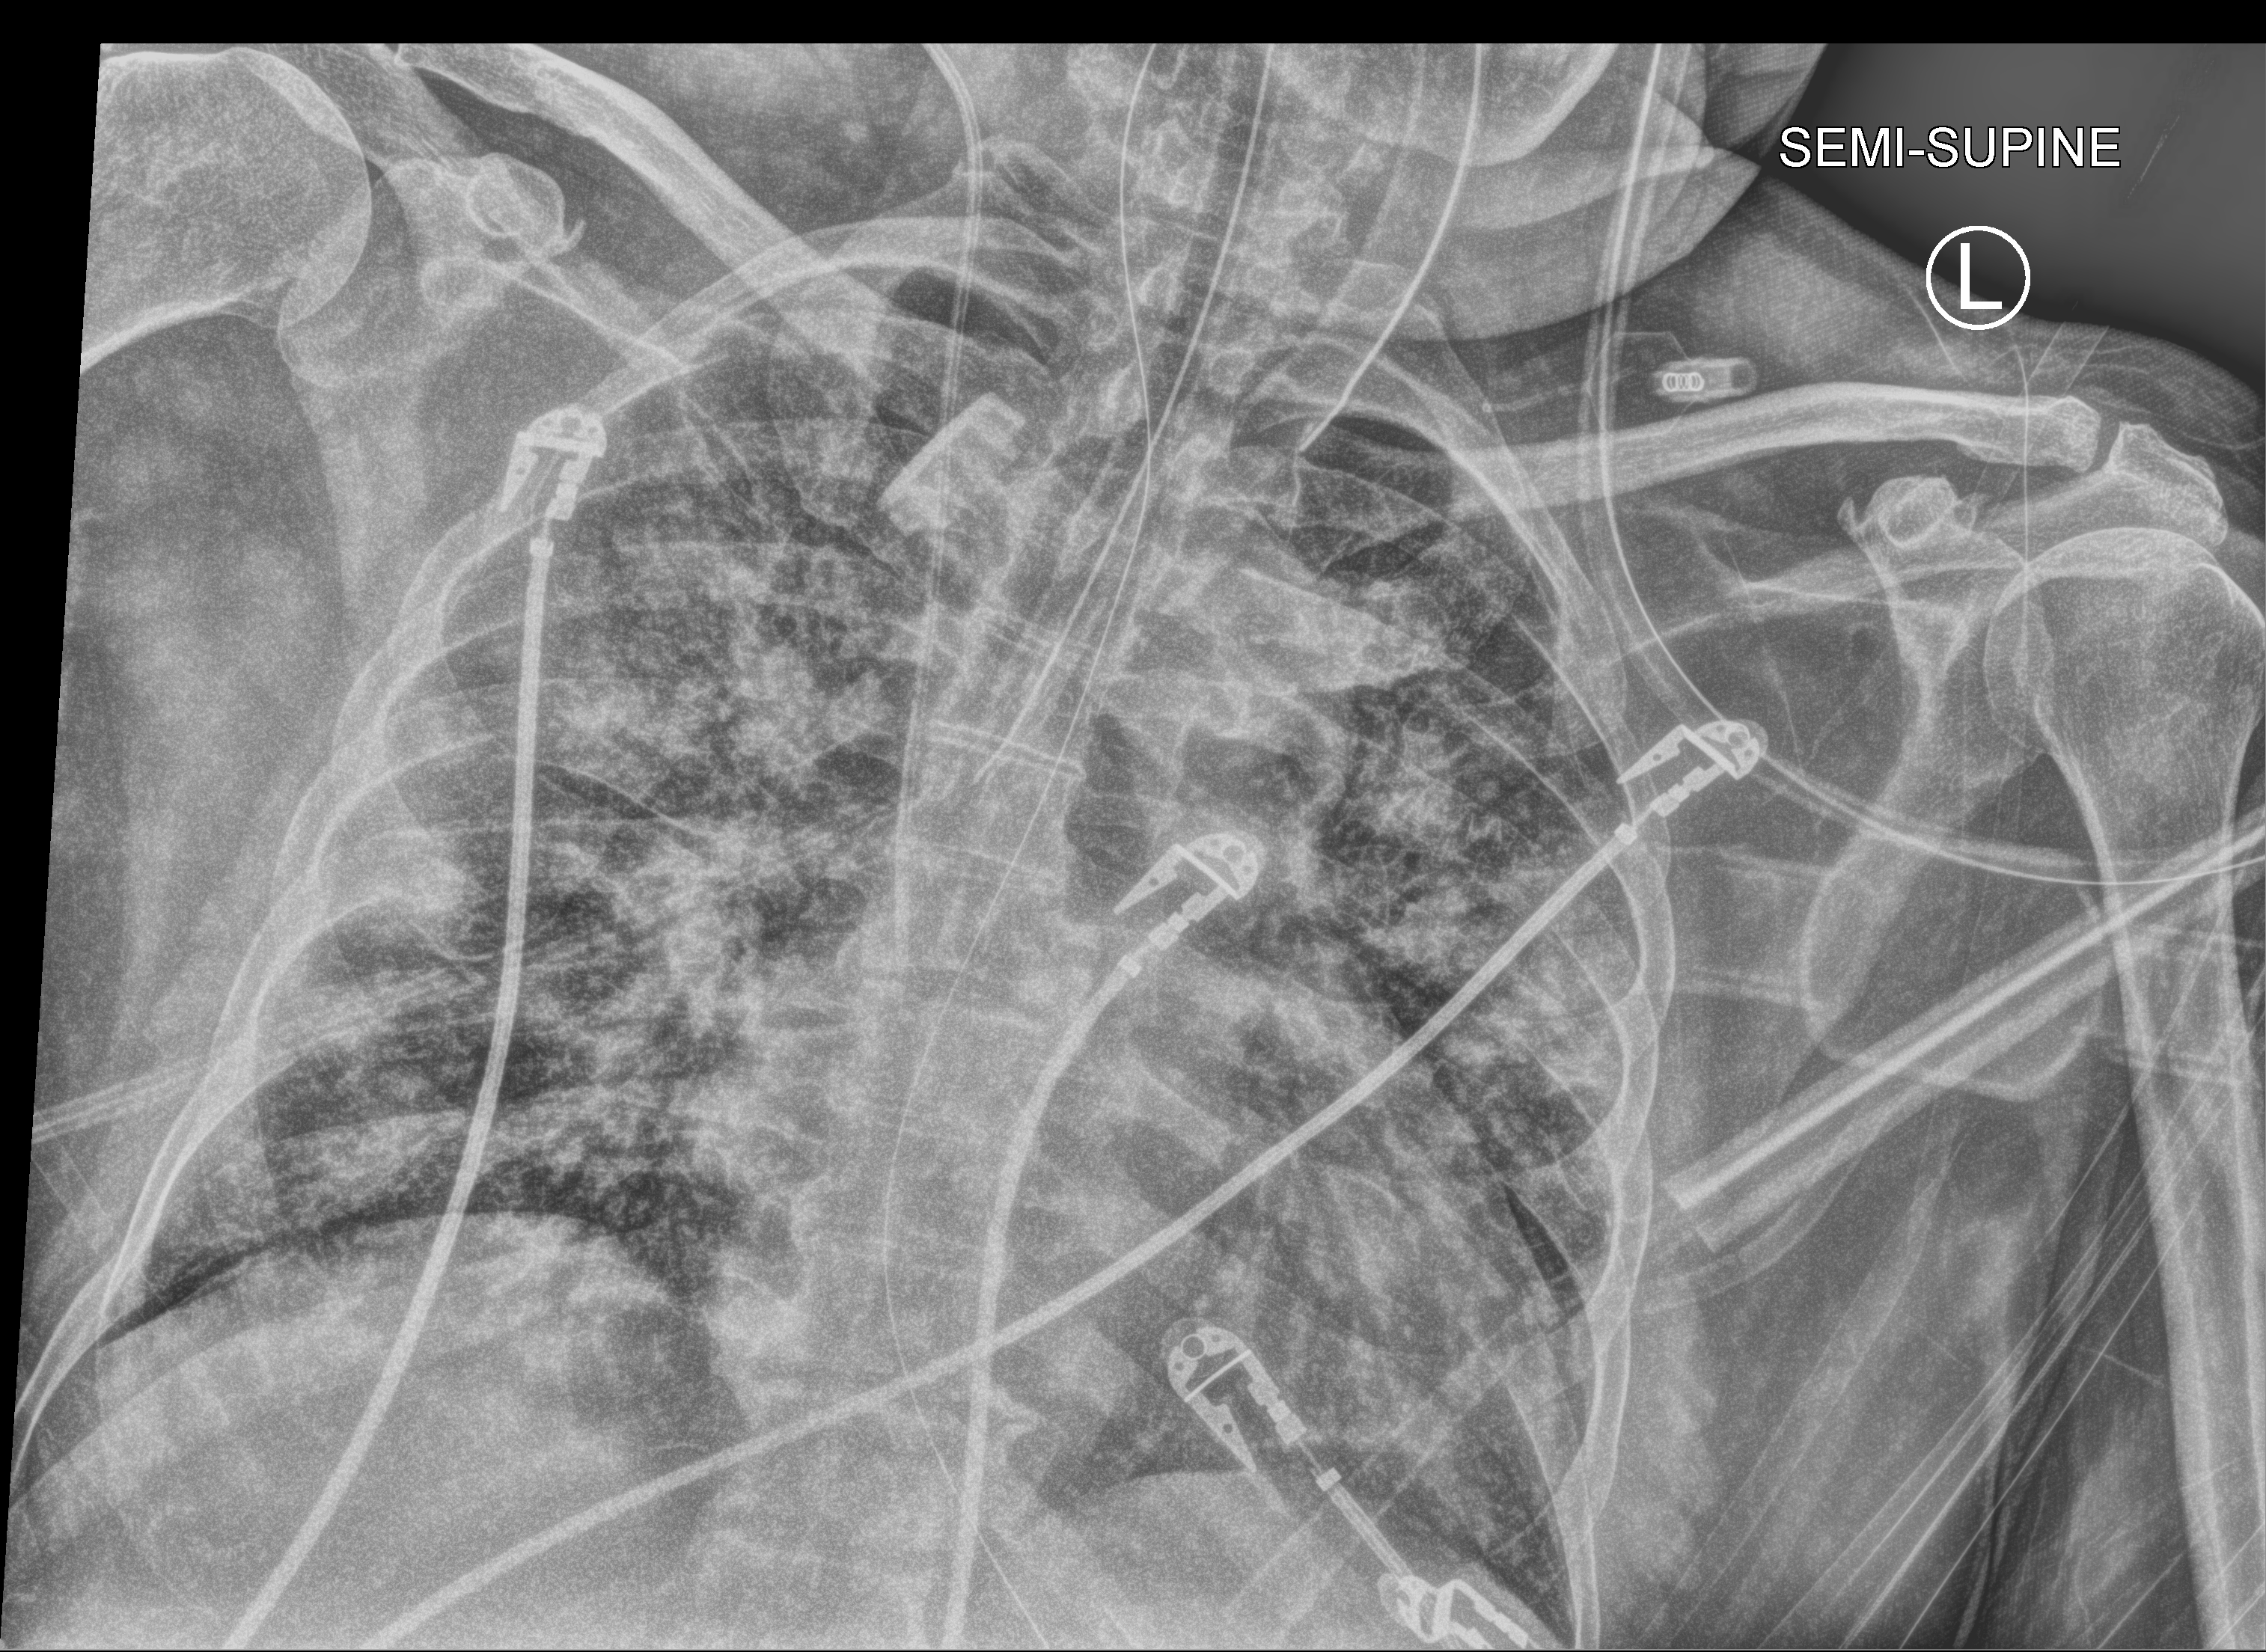
Portable chest radiograph; anteroposterior (AP) projection. Male patient hospitalised with COVID-19, age 60–74 years.
Admission-level facts for this patient (not findings on this image; timing relative to this image not recorded): mechanically ventilated during this hospital stay: yes; admitted to intensive care during this hospital stay: yes.